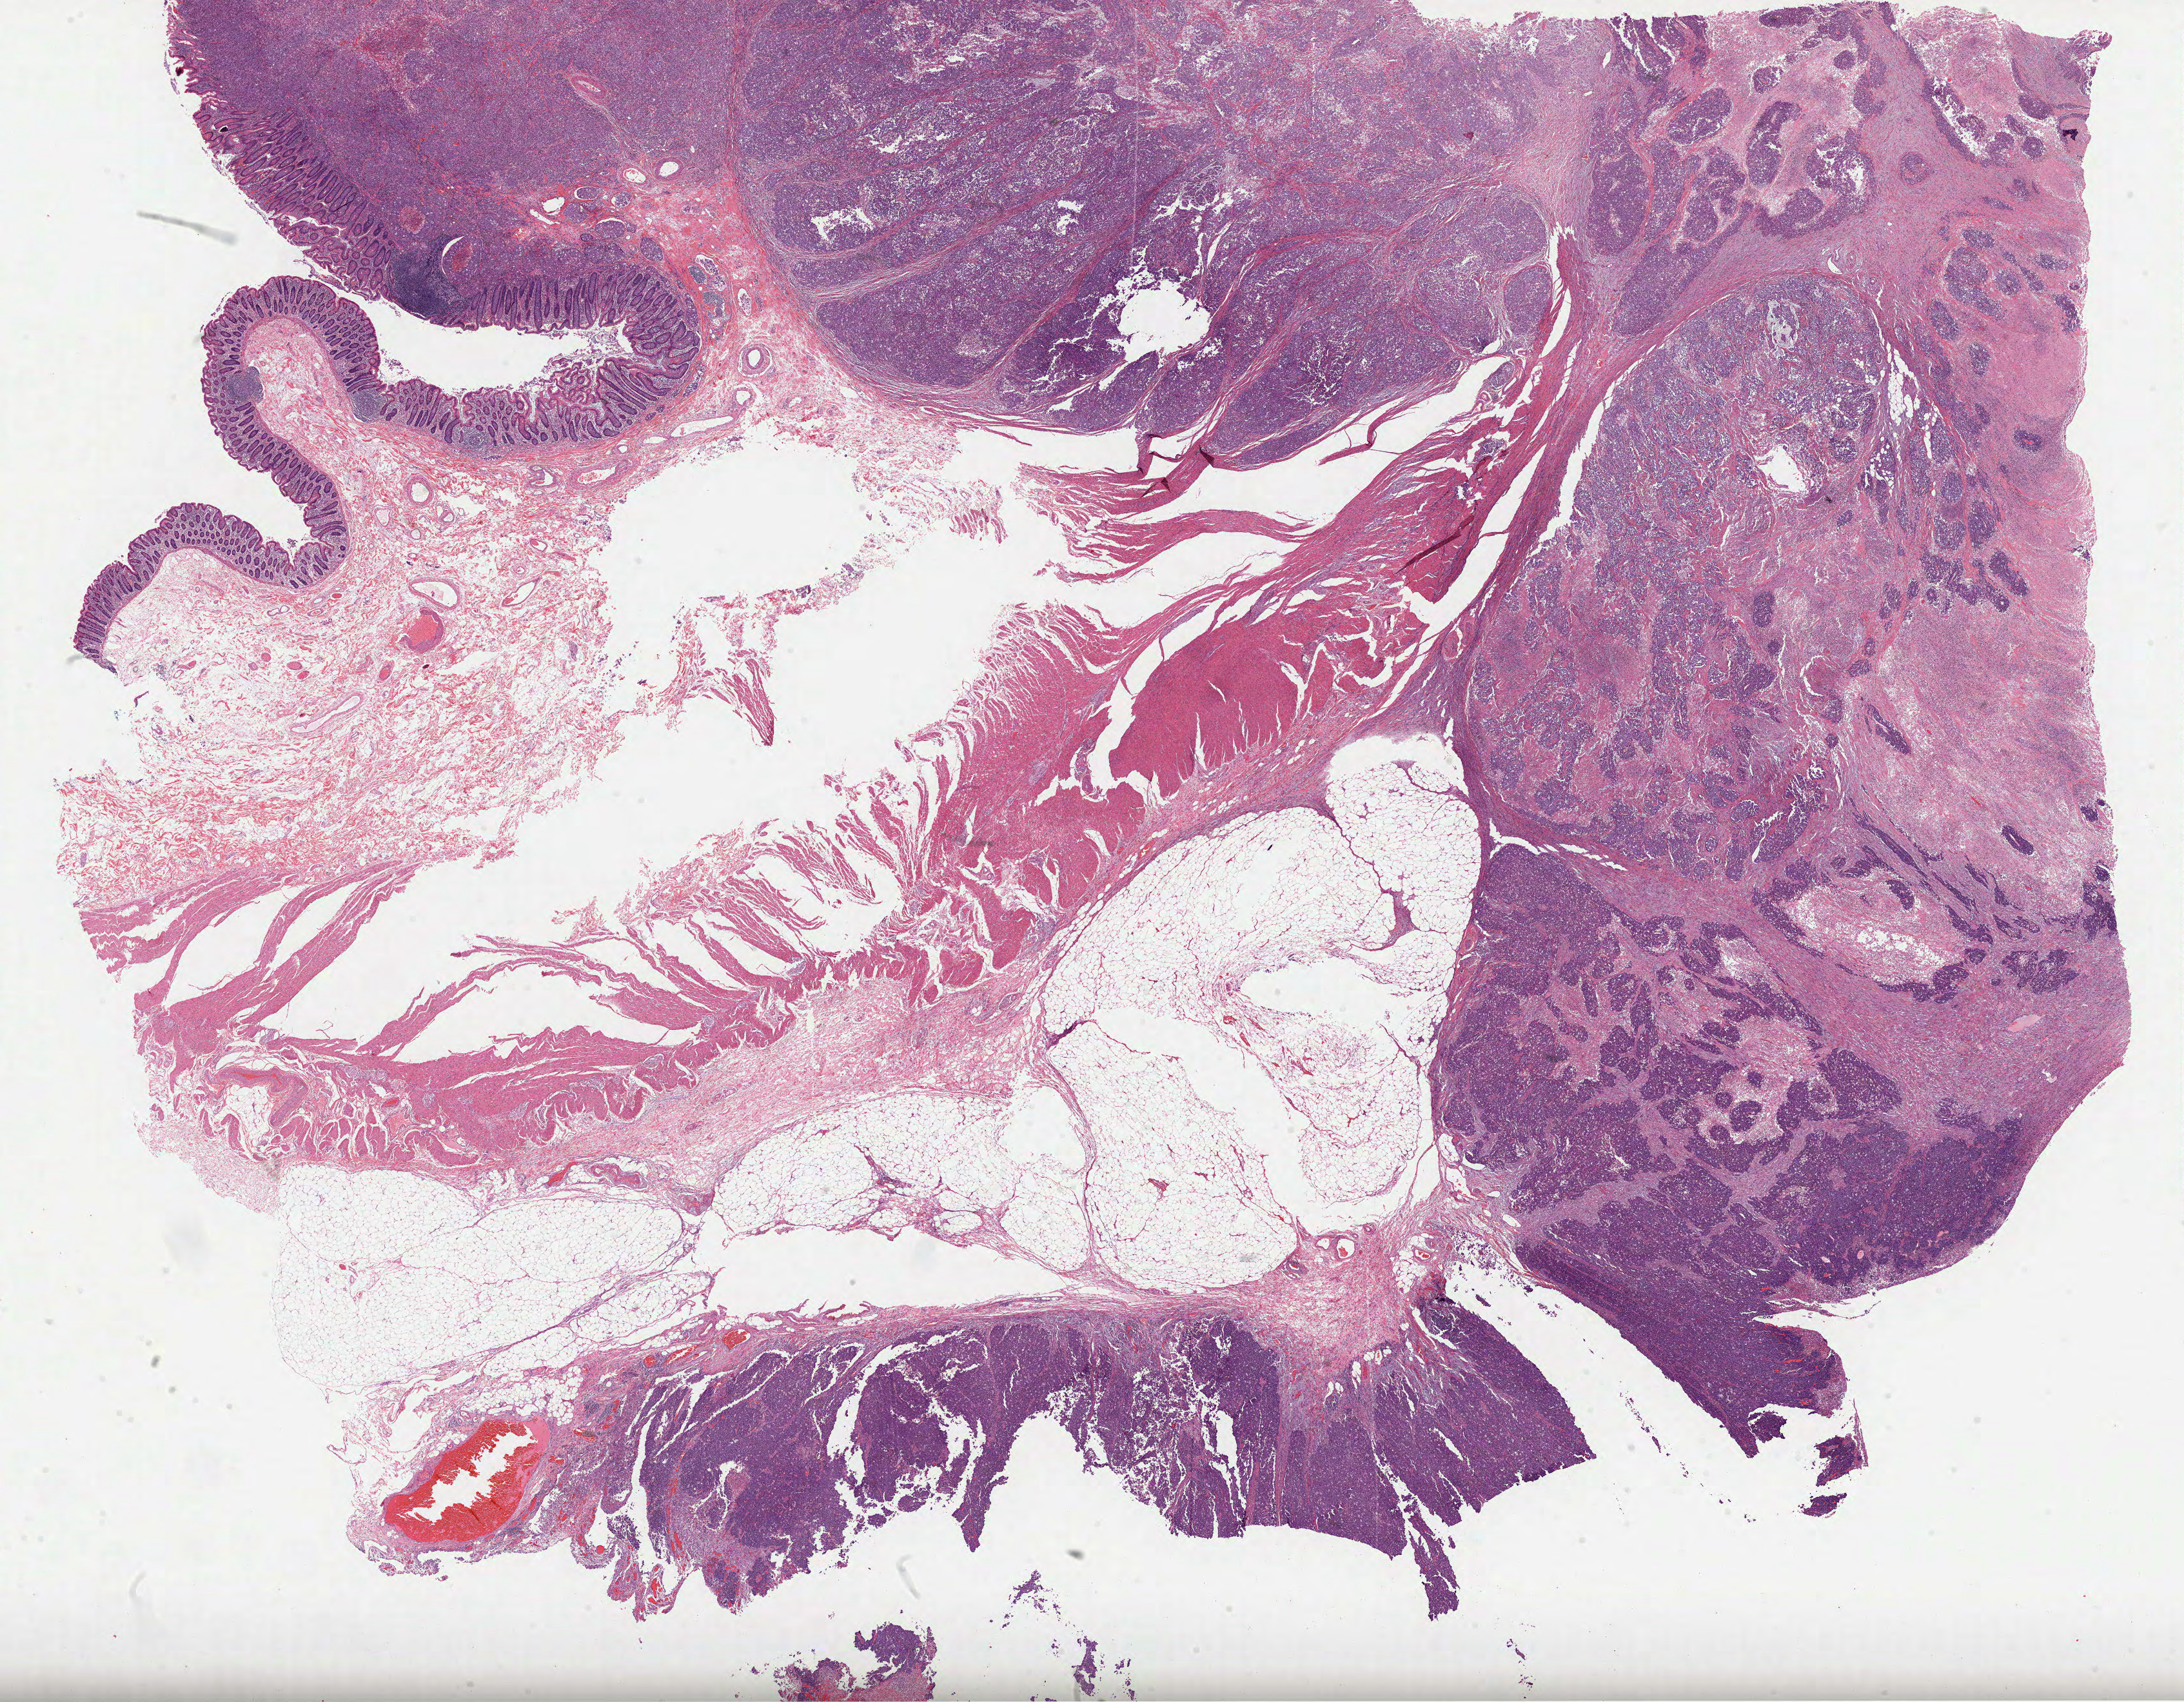
Digitized Hematoxylin and eosin (H&E) stained tissue section (whole slide), shown as a low-resolution overview of the whole scanned area (about 27.3 x 21.3 mm). FFPE section. Primary tumour sample from the colon. Patient: female, age at initial diagnosis 71 years.
Diagnosis: Adenocarcinoma, NOS (ascending colon). TNM: T1 N0 M0. AJCC pathologic stage: I (6th edition).